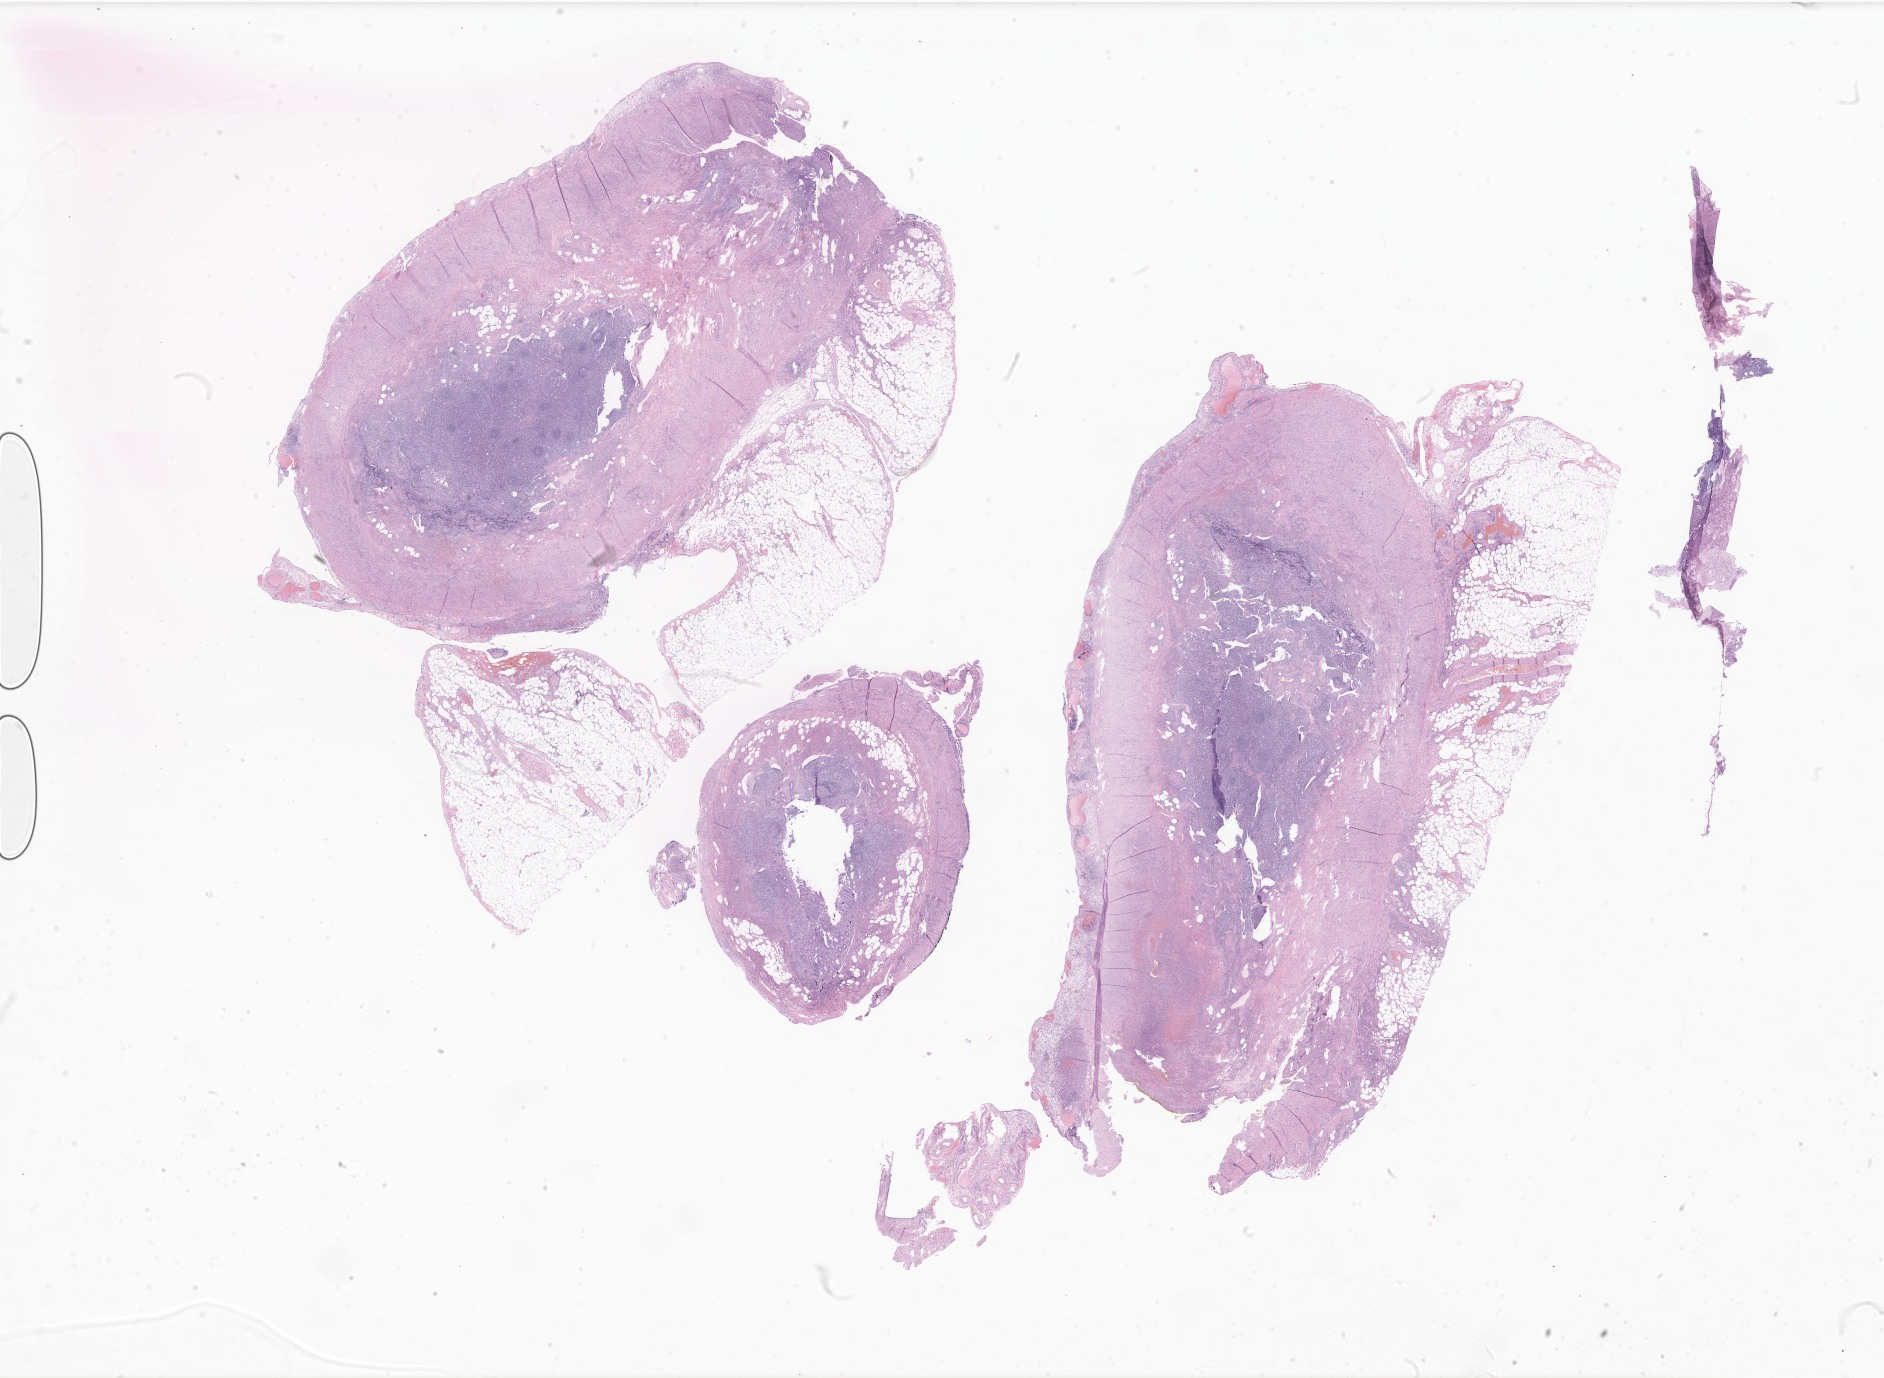
Whole-slide image, H&E stain of tumor tissue from the appendix, a low-resolution overview of the entire scanned area, about 31.8 x 23.2 mm, formalin-fixed, paraffin-embedded (FFPE) tissue. Female patient, age 204 months (17 years).
• diagnosis (ICD-O-3 morphology term): Carcinoid tumor of uncertain malignant potential